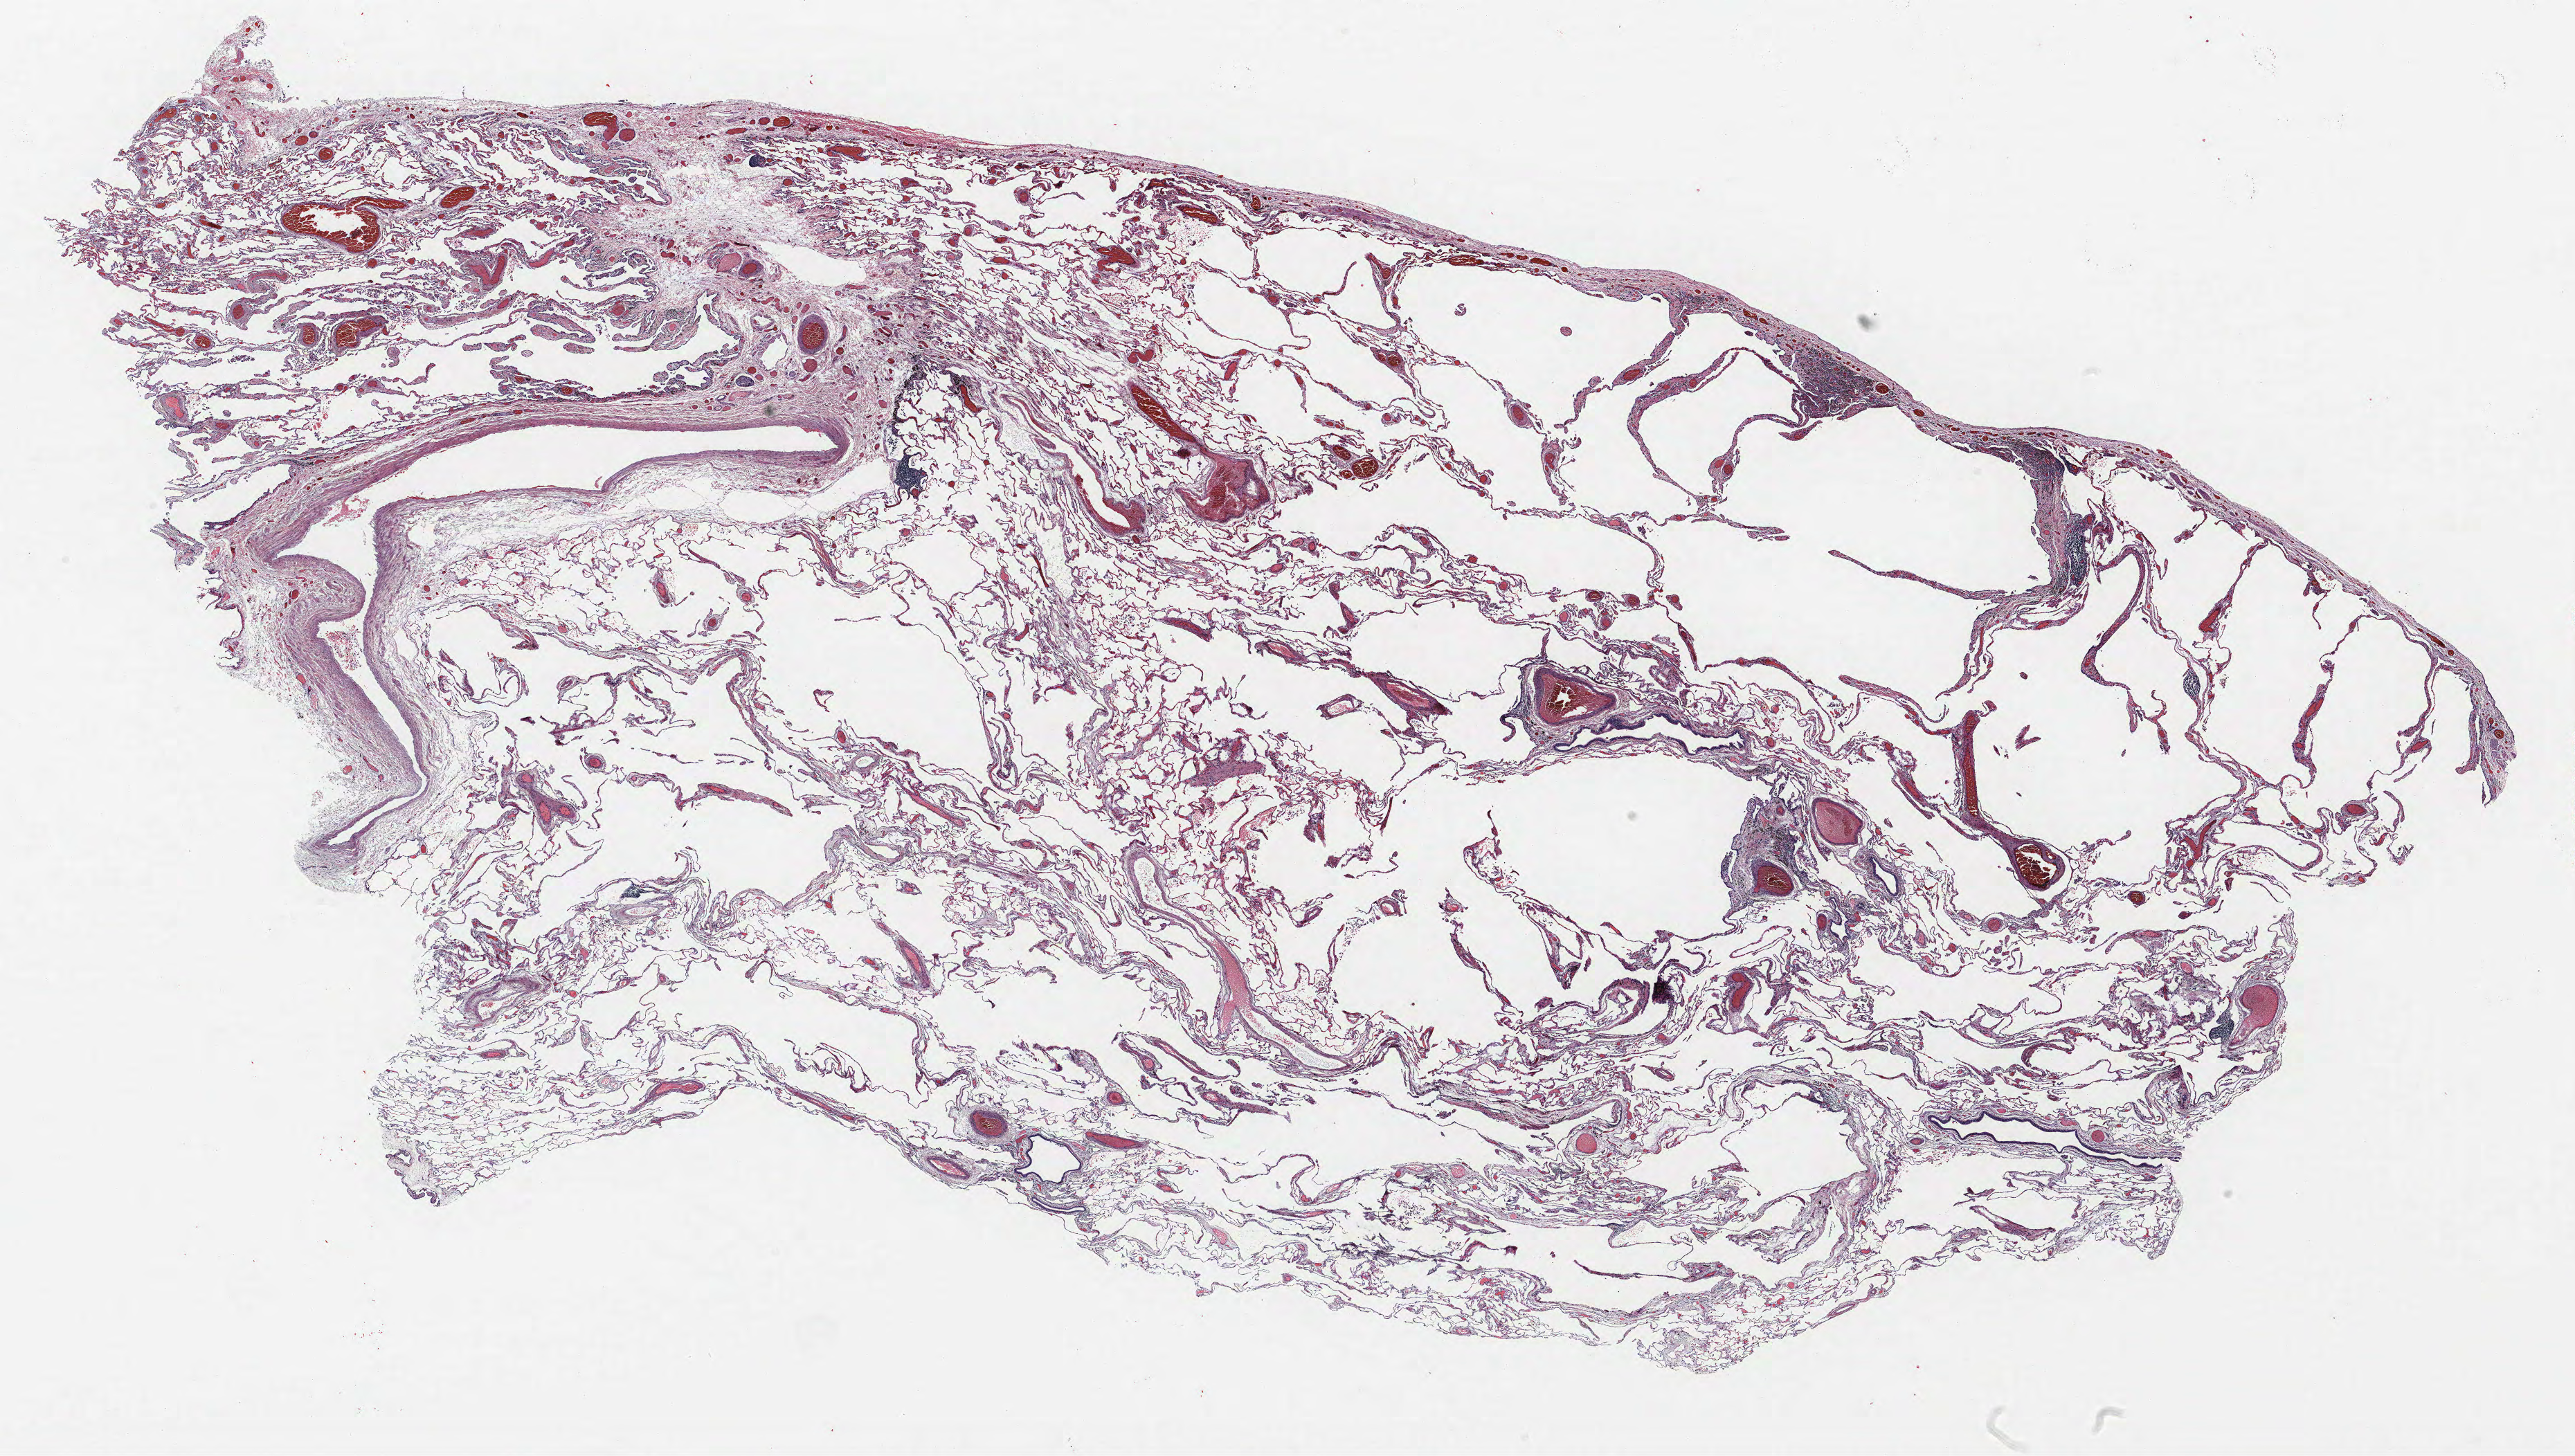
Whole-slide histology image, H&E-stained — low-resolution overview of the scanned area, about 29.8 x 16.8 mm (slide scanned at 40x), FFPE section, lung. Male, age 62 at enrolment. Current smoker at enrolment. Grade: moderately differentiated (G2).
Primary tumour location (clinical record): left upper lobe. Tumour size (pathology): 17 mm. Participant's lung-cancer diagnosis: Squamous cell carcinoma, NOS. Stage (AJCC 6th edition): IA.